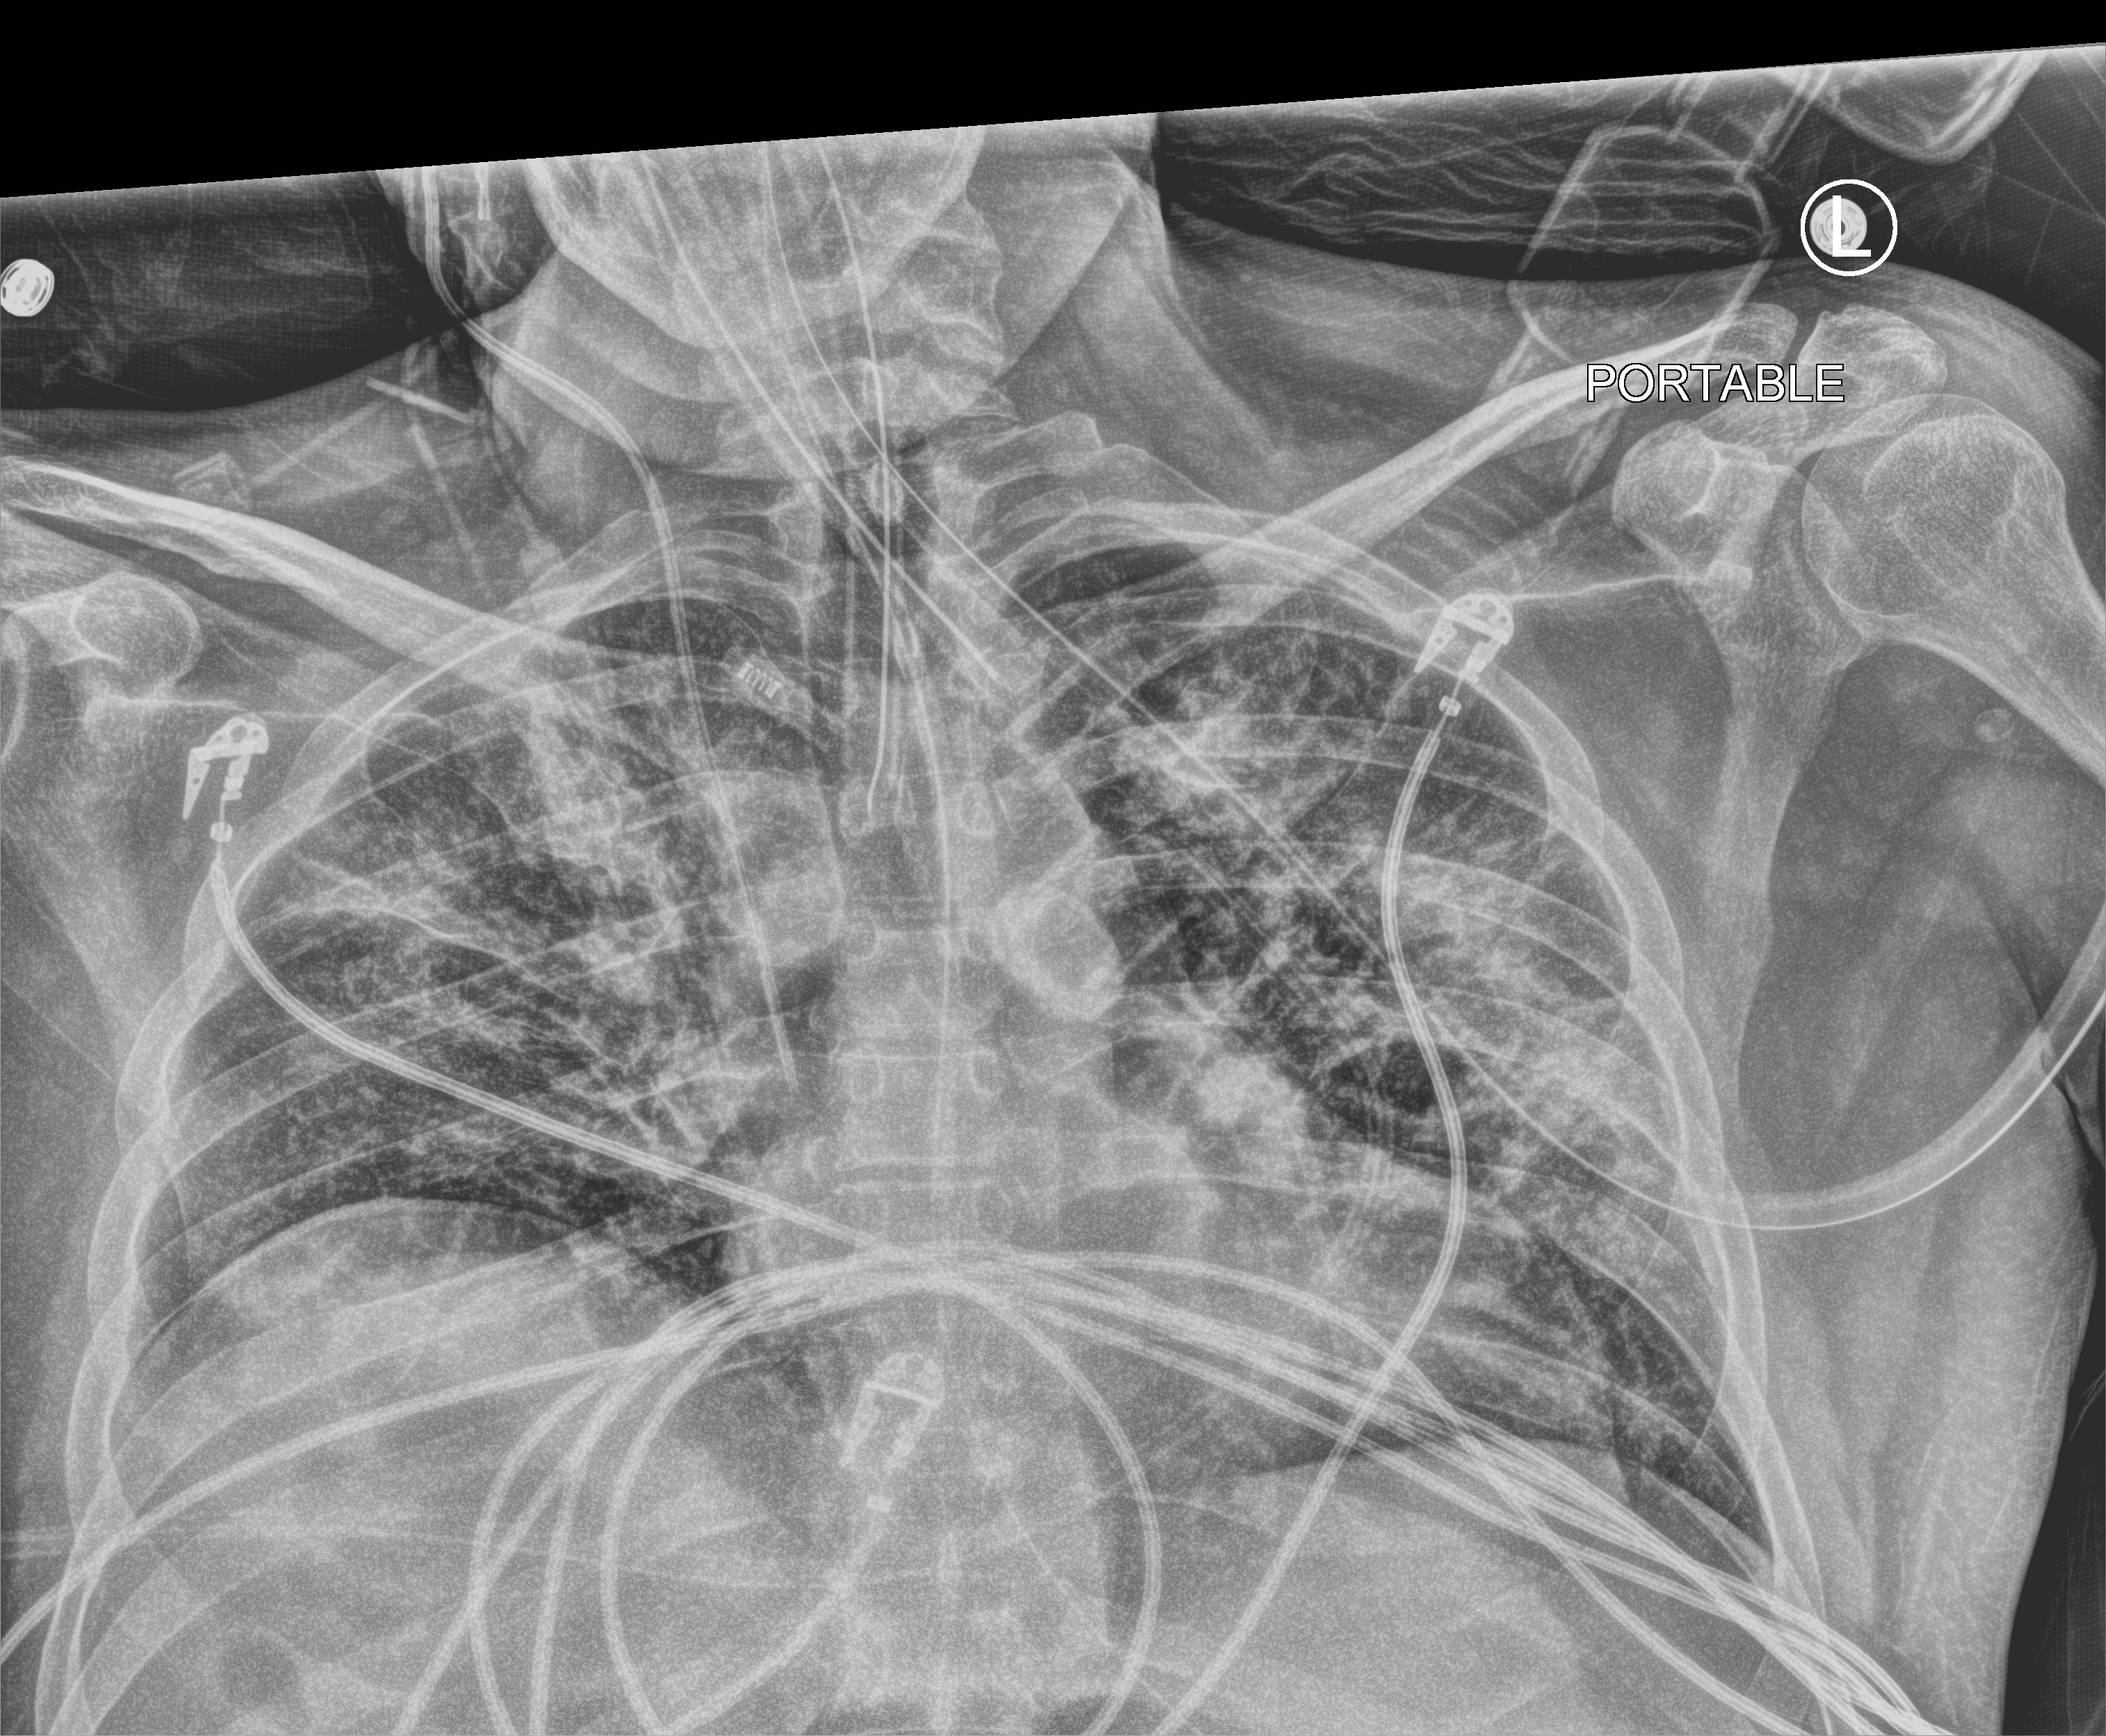
Portable chest radiograph, anteroposterior (AP) projection. Patient hospitalised with COVID-19; male, aged 18–59 years.
Admission-level facts for this patient (not findings on this image; timing relative to this image not recorded):
- admitted to intensive care during this hospital stay: yes
- mechanically ventilated during this hospital stay: yes